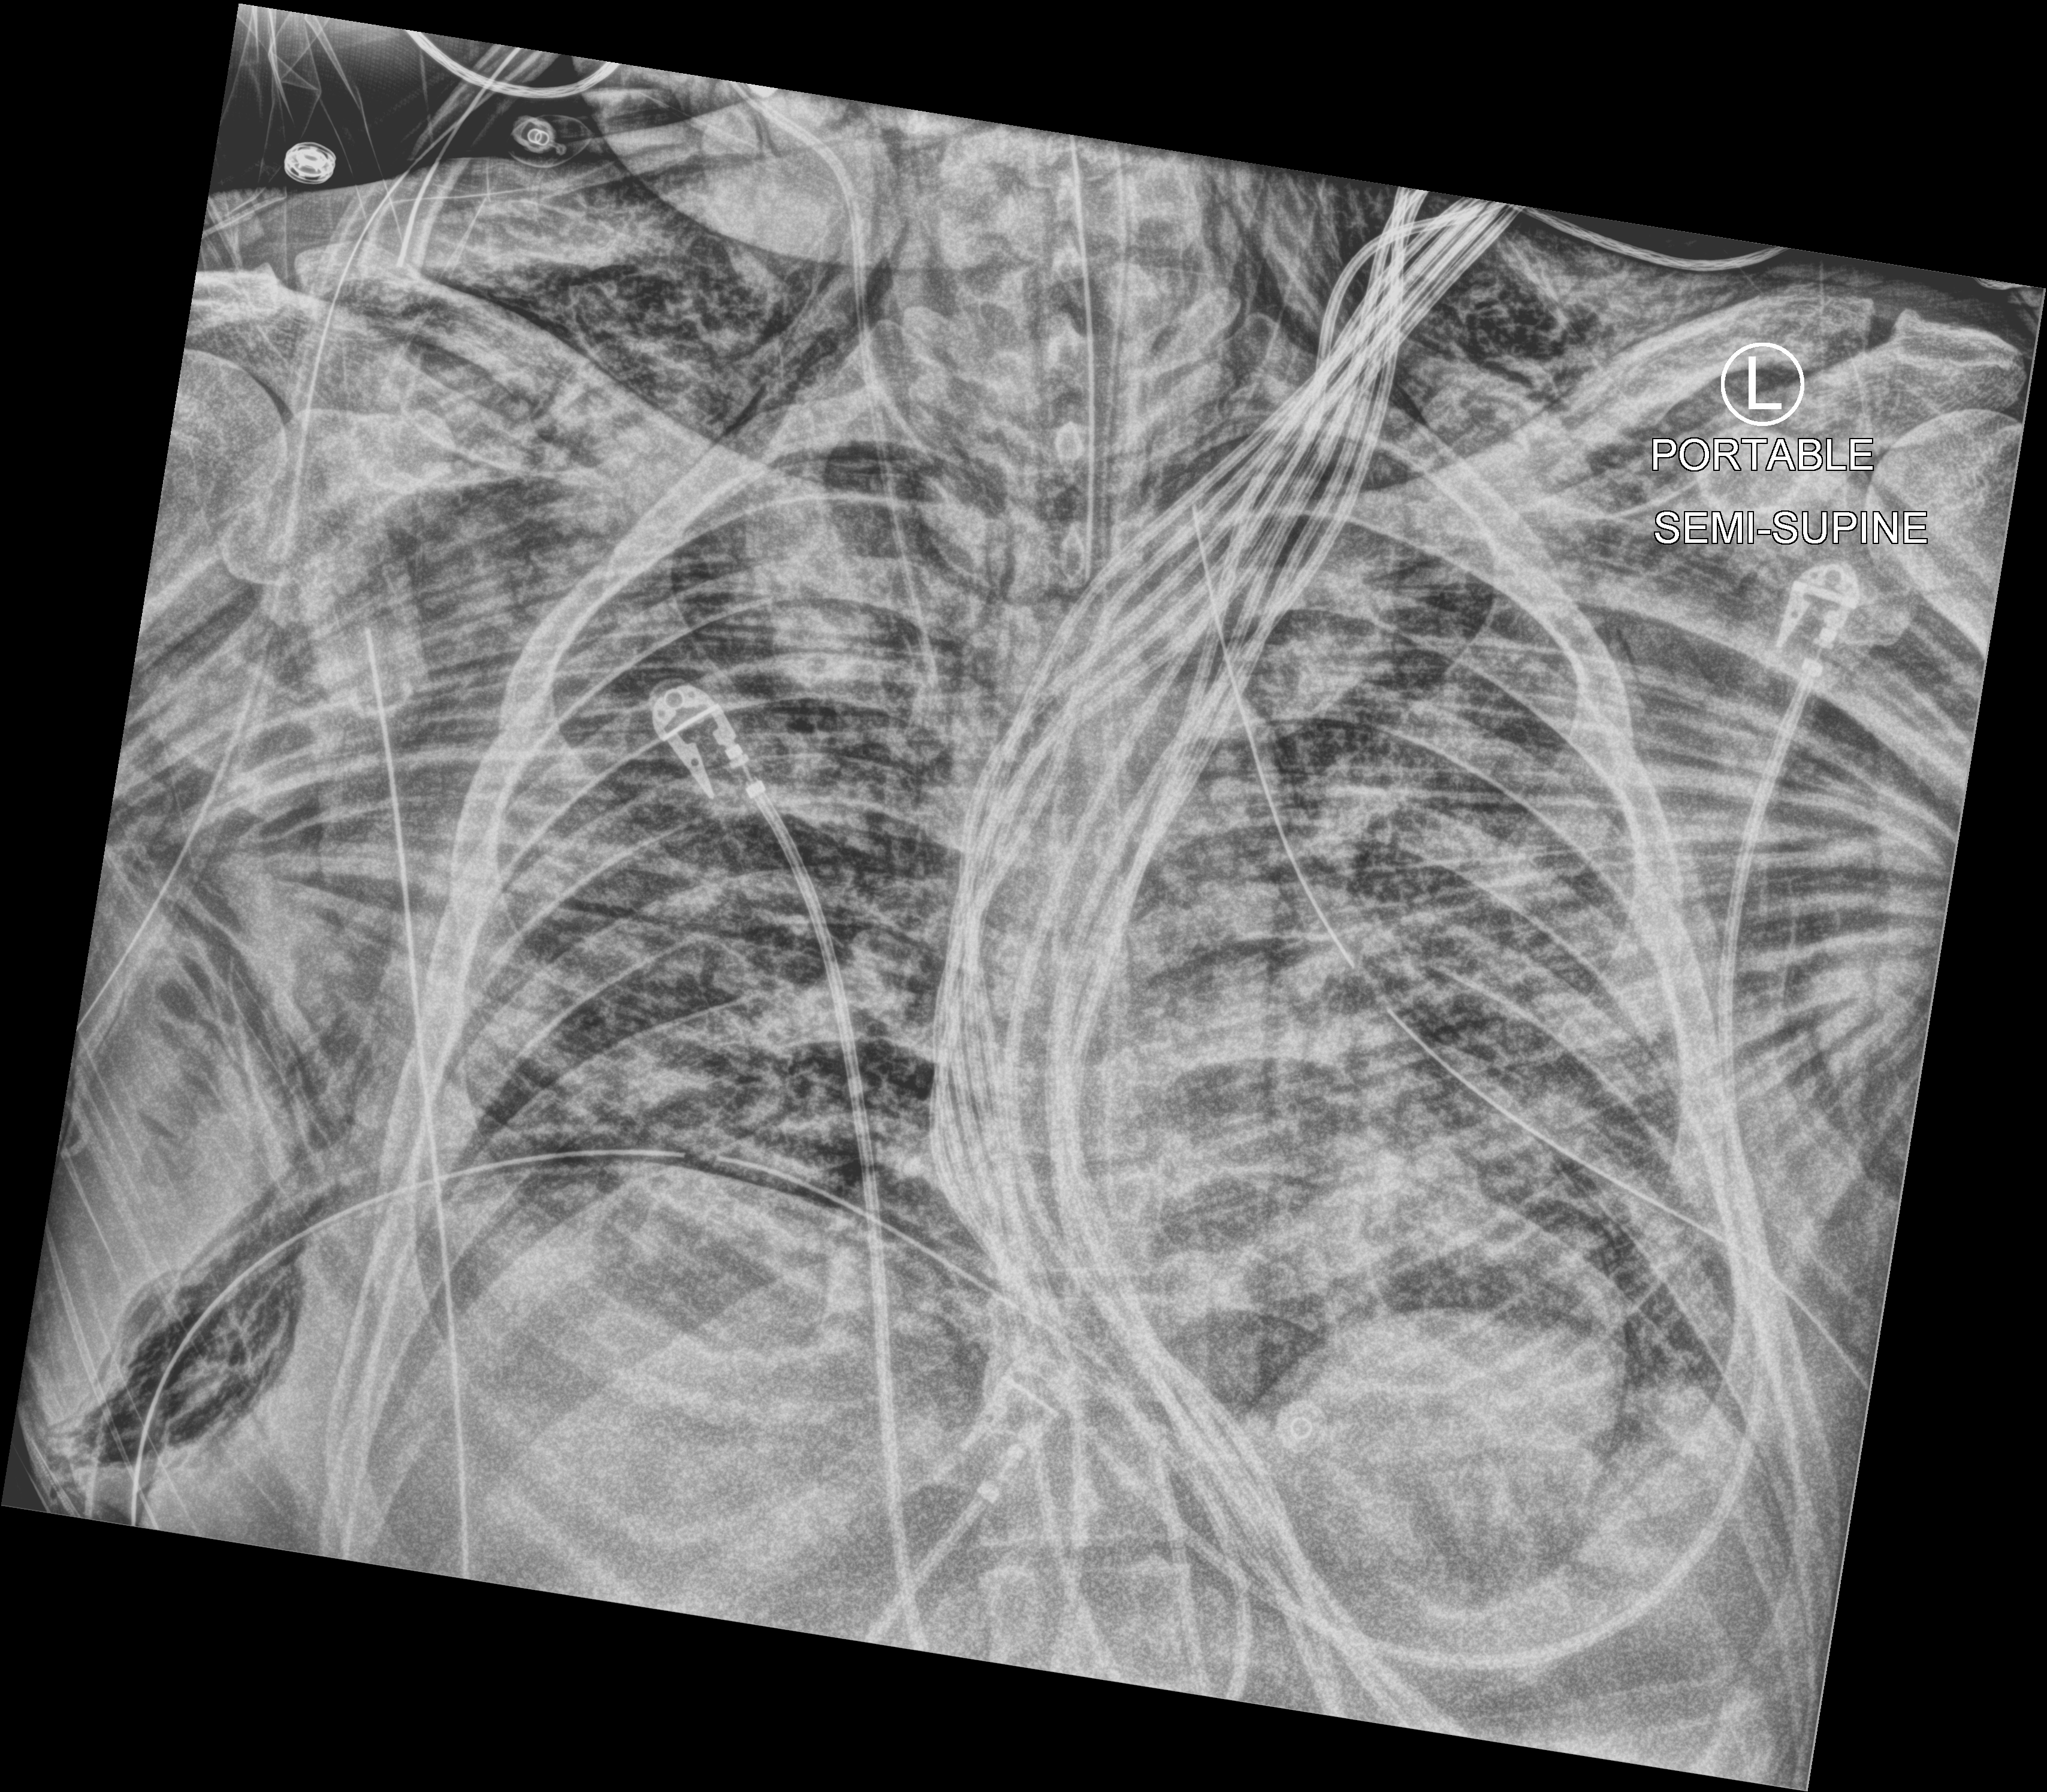
Chest X-ray (portable); anteroposterior (AP) projection. Male patient hospitalised with COVID-19, age 18–59 years.
Hospital-stay facts (about this admission, not read from this image; timing relative to this image not recorded):
- mechanically ventilated during this hospital stay: yes